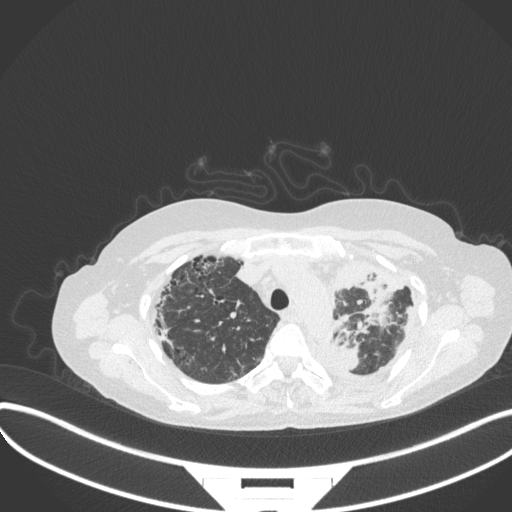
Chest CT, one axial slice; position 266 of 373 along the scan axis; reconstruction kernel B31f; lung window (W 1500 / L -600 HU); 1 mm slice thickness; 512 × 512 image matrix, field of view 400 × 400 mm. Female patient, age 56 years. From the clinical record (not read from this slice): clinical TNM (as recorded): T1 N0 M0.
Outlined on this slice (rectangle marked by the reading radiologist):
- lung tumour (recorded histology: adenocarcinoma): bounding box [x1, y1, x2, y2] px = [358, 267, 401, 330]